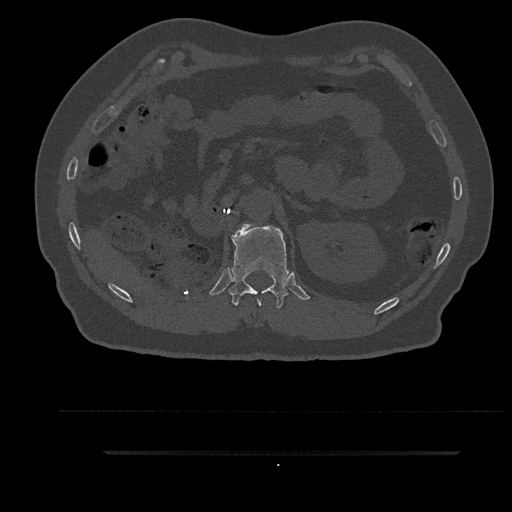
CT including the spine, one axial slice. Slice 241 of 797 in the series (ordered by position). Reconstruction kernel Br40s/3. 120 kVp. Bone window (W 1800 / L 400 HU). 0.5 mm slice thickness. 512 × 512 image matrix. Male patient, age 63 years. Case-level facts recorded for this patient, not image findings: primary cancer: renal.
Annotated regions visible in this slice (semi-automatic segmentation, software-assisted and operator-edited):
- T12 vertebra: bounding box [x1, y1, x2, y2] px = [229, 224, 289, 309]